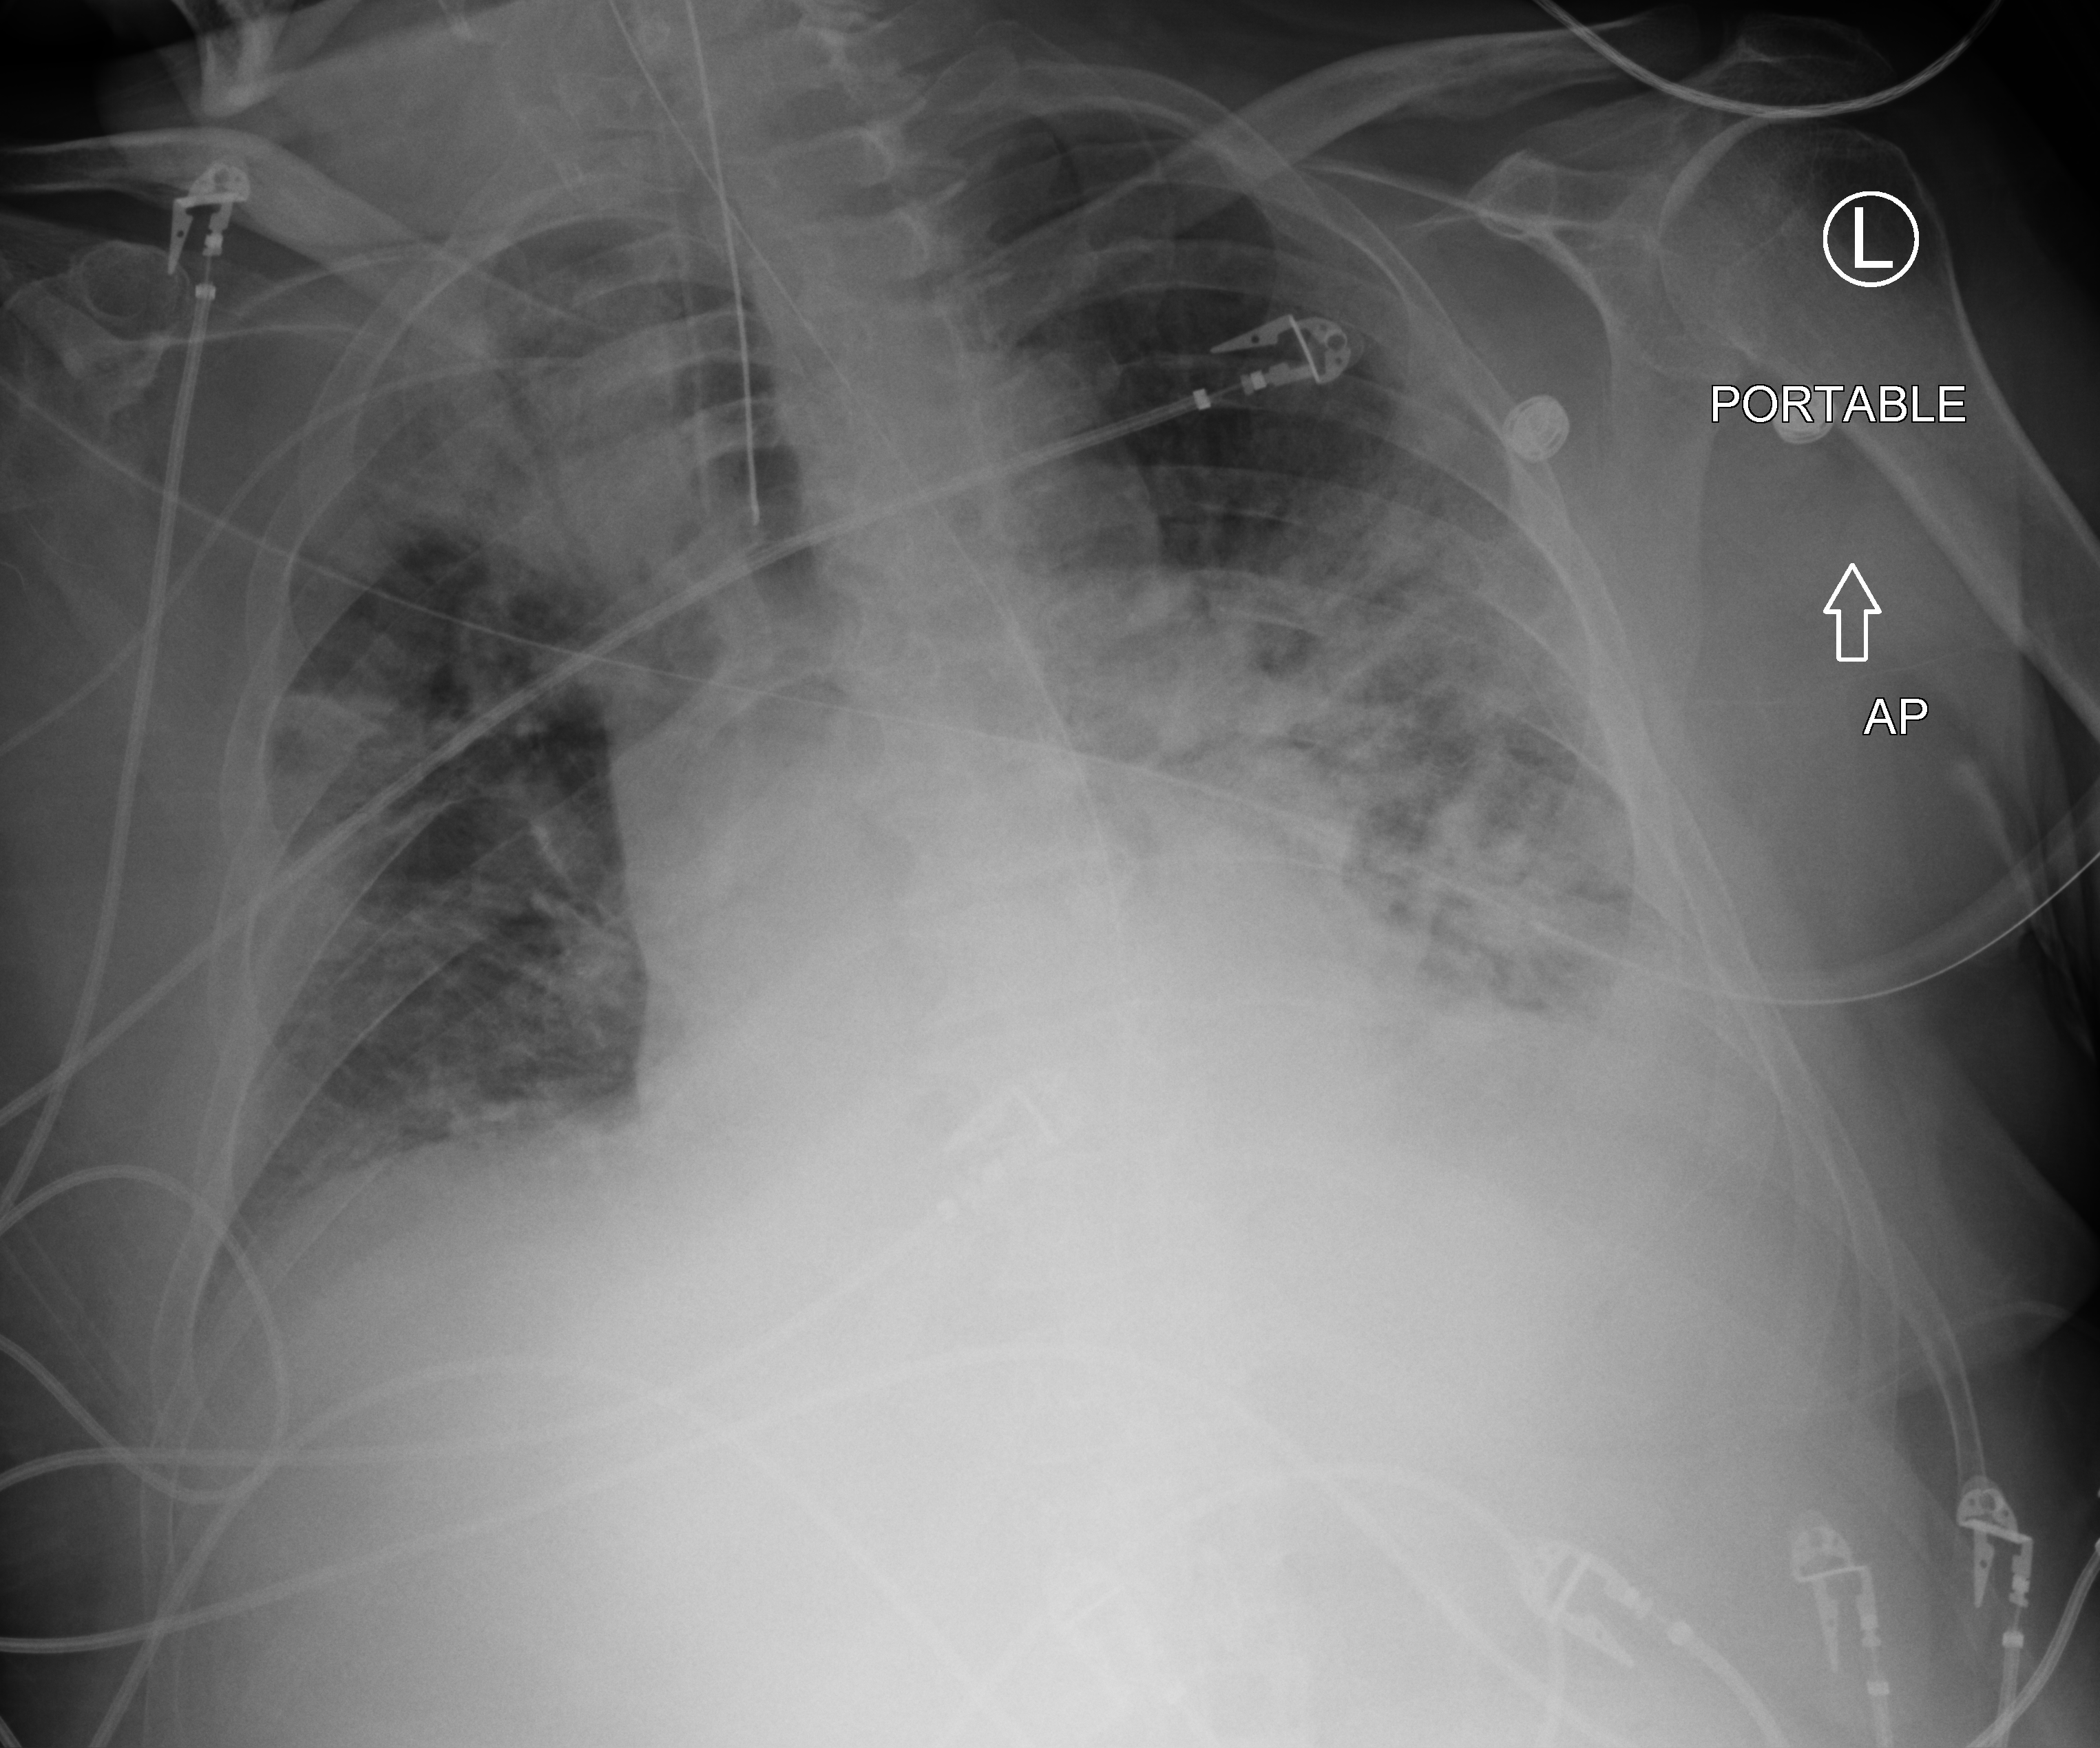
Chest X-ray (portable). Male patient hospitalised with COVID-19, age 60–74 years.
Admission-level facts for this patient (not findings on this image; timing relative to this image not recorded):
- COPD (admission record): no
- diabetes (admission record): no